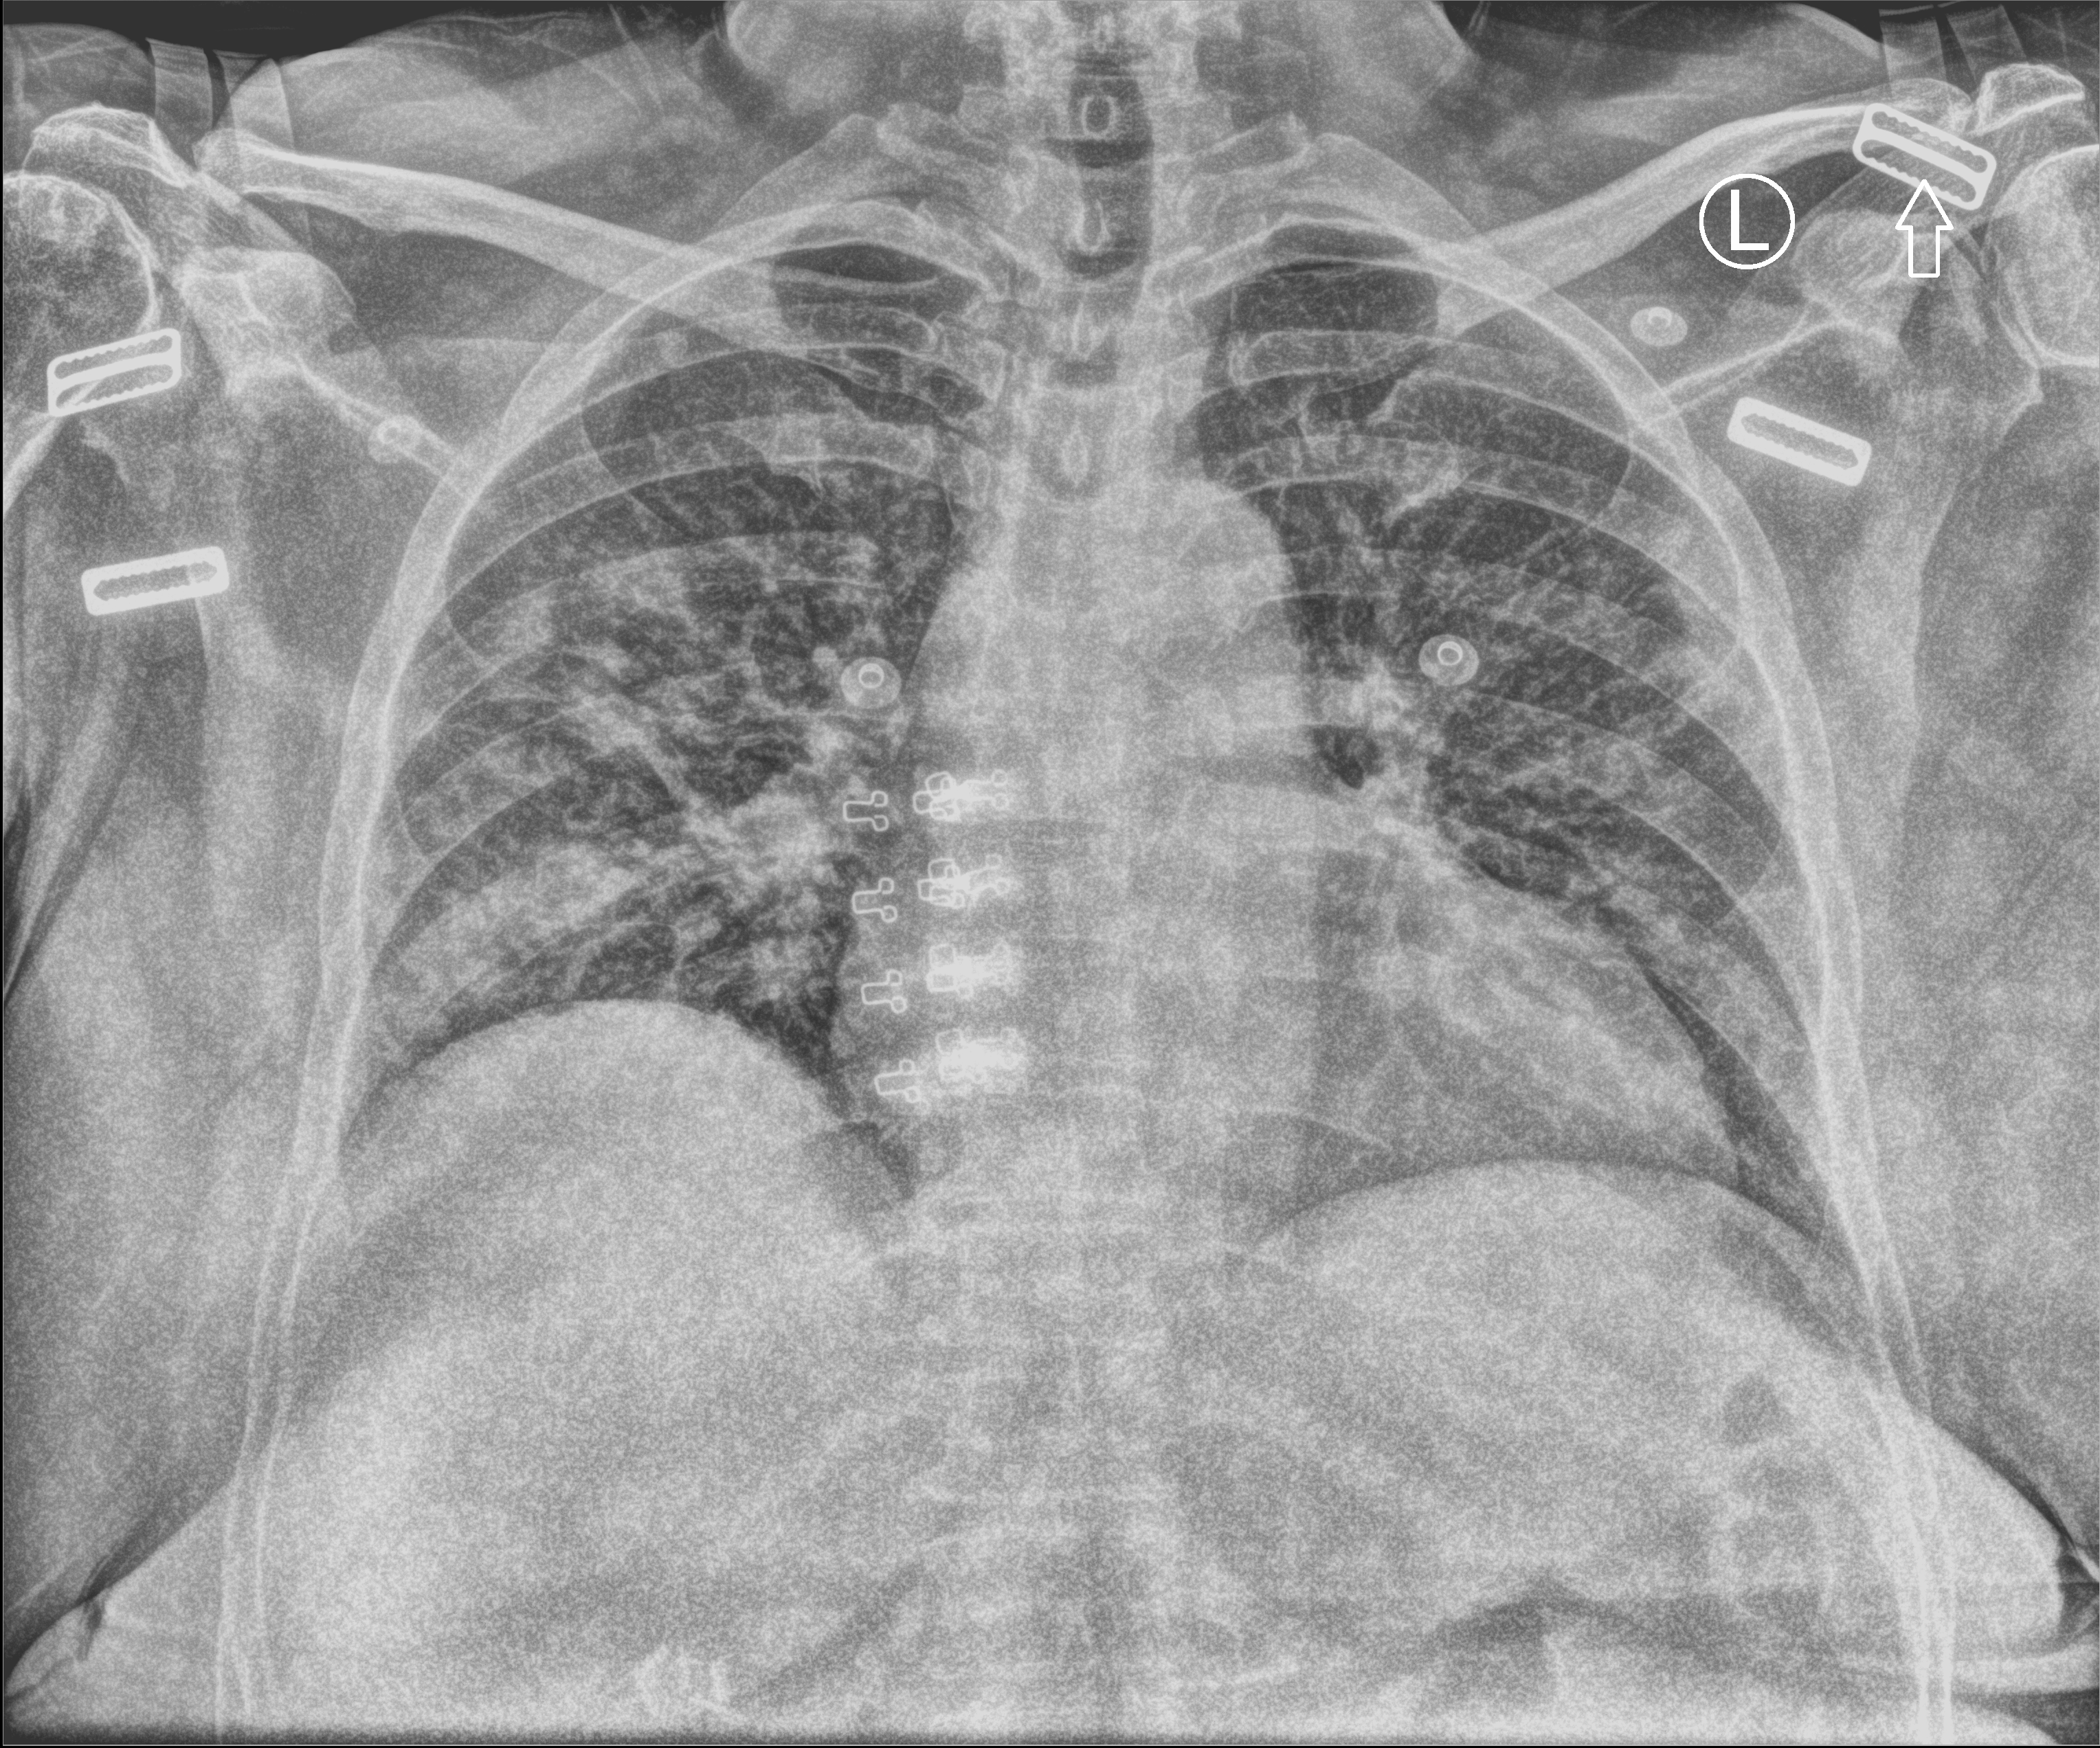
Chest X-ray (portable). Patient hospitalised with COVID-19; female, aged 60–74 years.
From the hospital-stay record, not from the radiograph (when in the stay this image was taken is not recorded):
- length of hospital stay: 7 days
- COPD (admission record): no